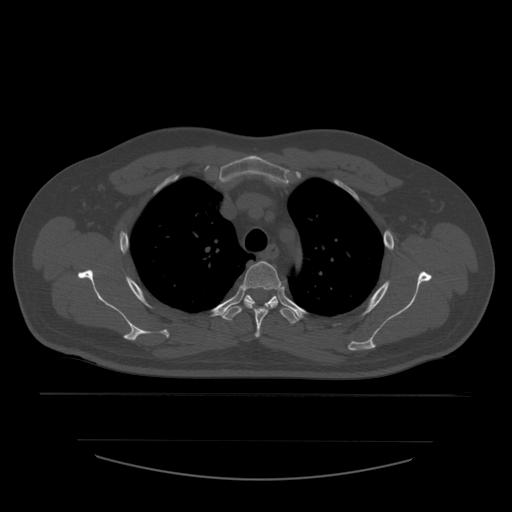
CT including the spine, one axial slice. Slice 427 of 532 in the series (ordered by position). Reconstruction kernel STANDARD. 120 kVp. Bone window (W 1800 / L 400 HU). 512 × 512 image matrix. Patient age 44 years. From the clinical record (not read from this slice): primary cancer: soft tissue sarcoma.
Annotated regions visible in this slice (semi-automatically segmented with operator editing):
- T3 vertebra: bounding box <242,261,282,338> (left, top, right, bottom; pixels)
- T4 vertebra: <221,295,299,324>